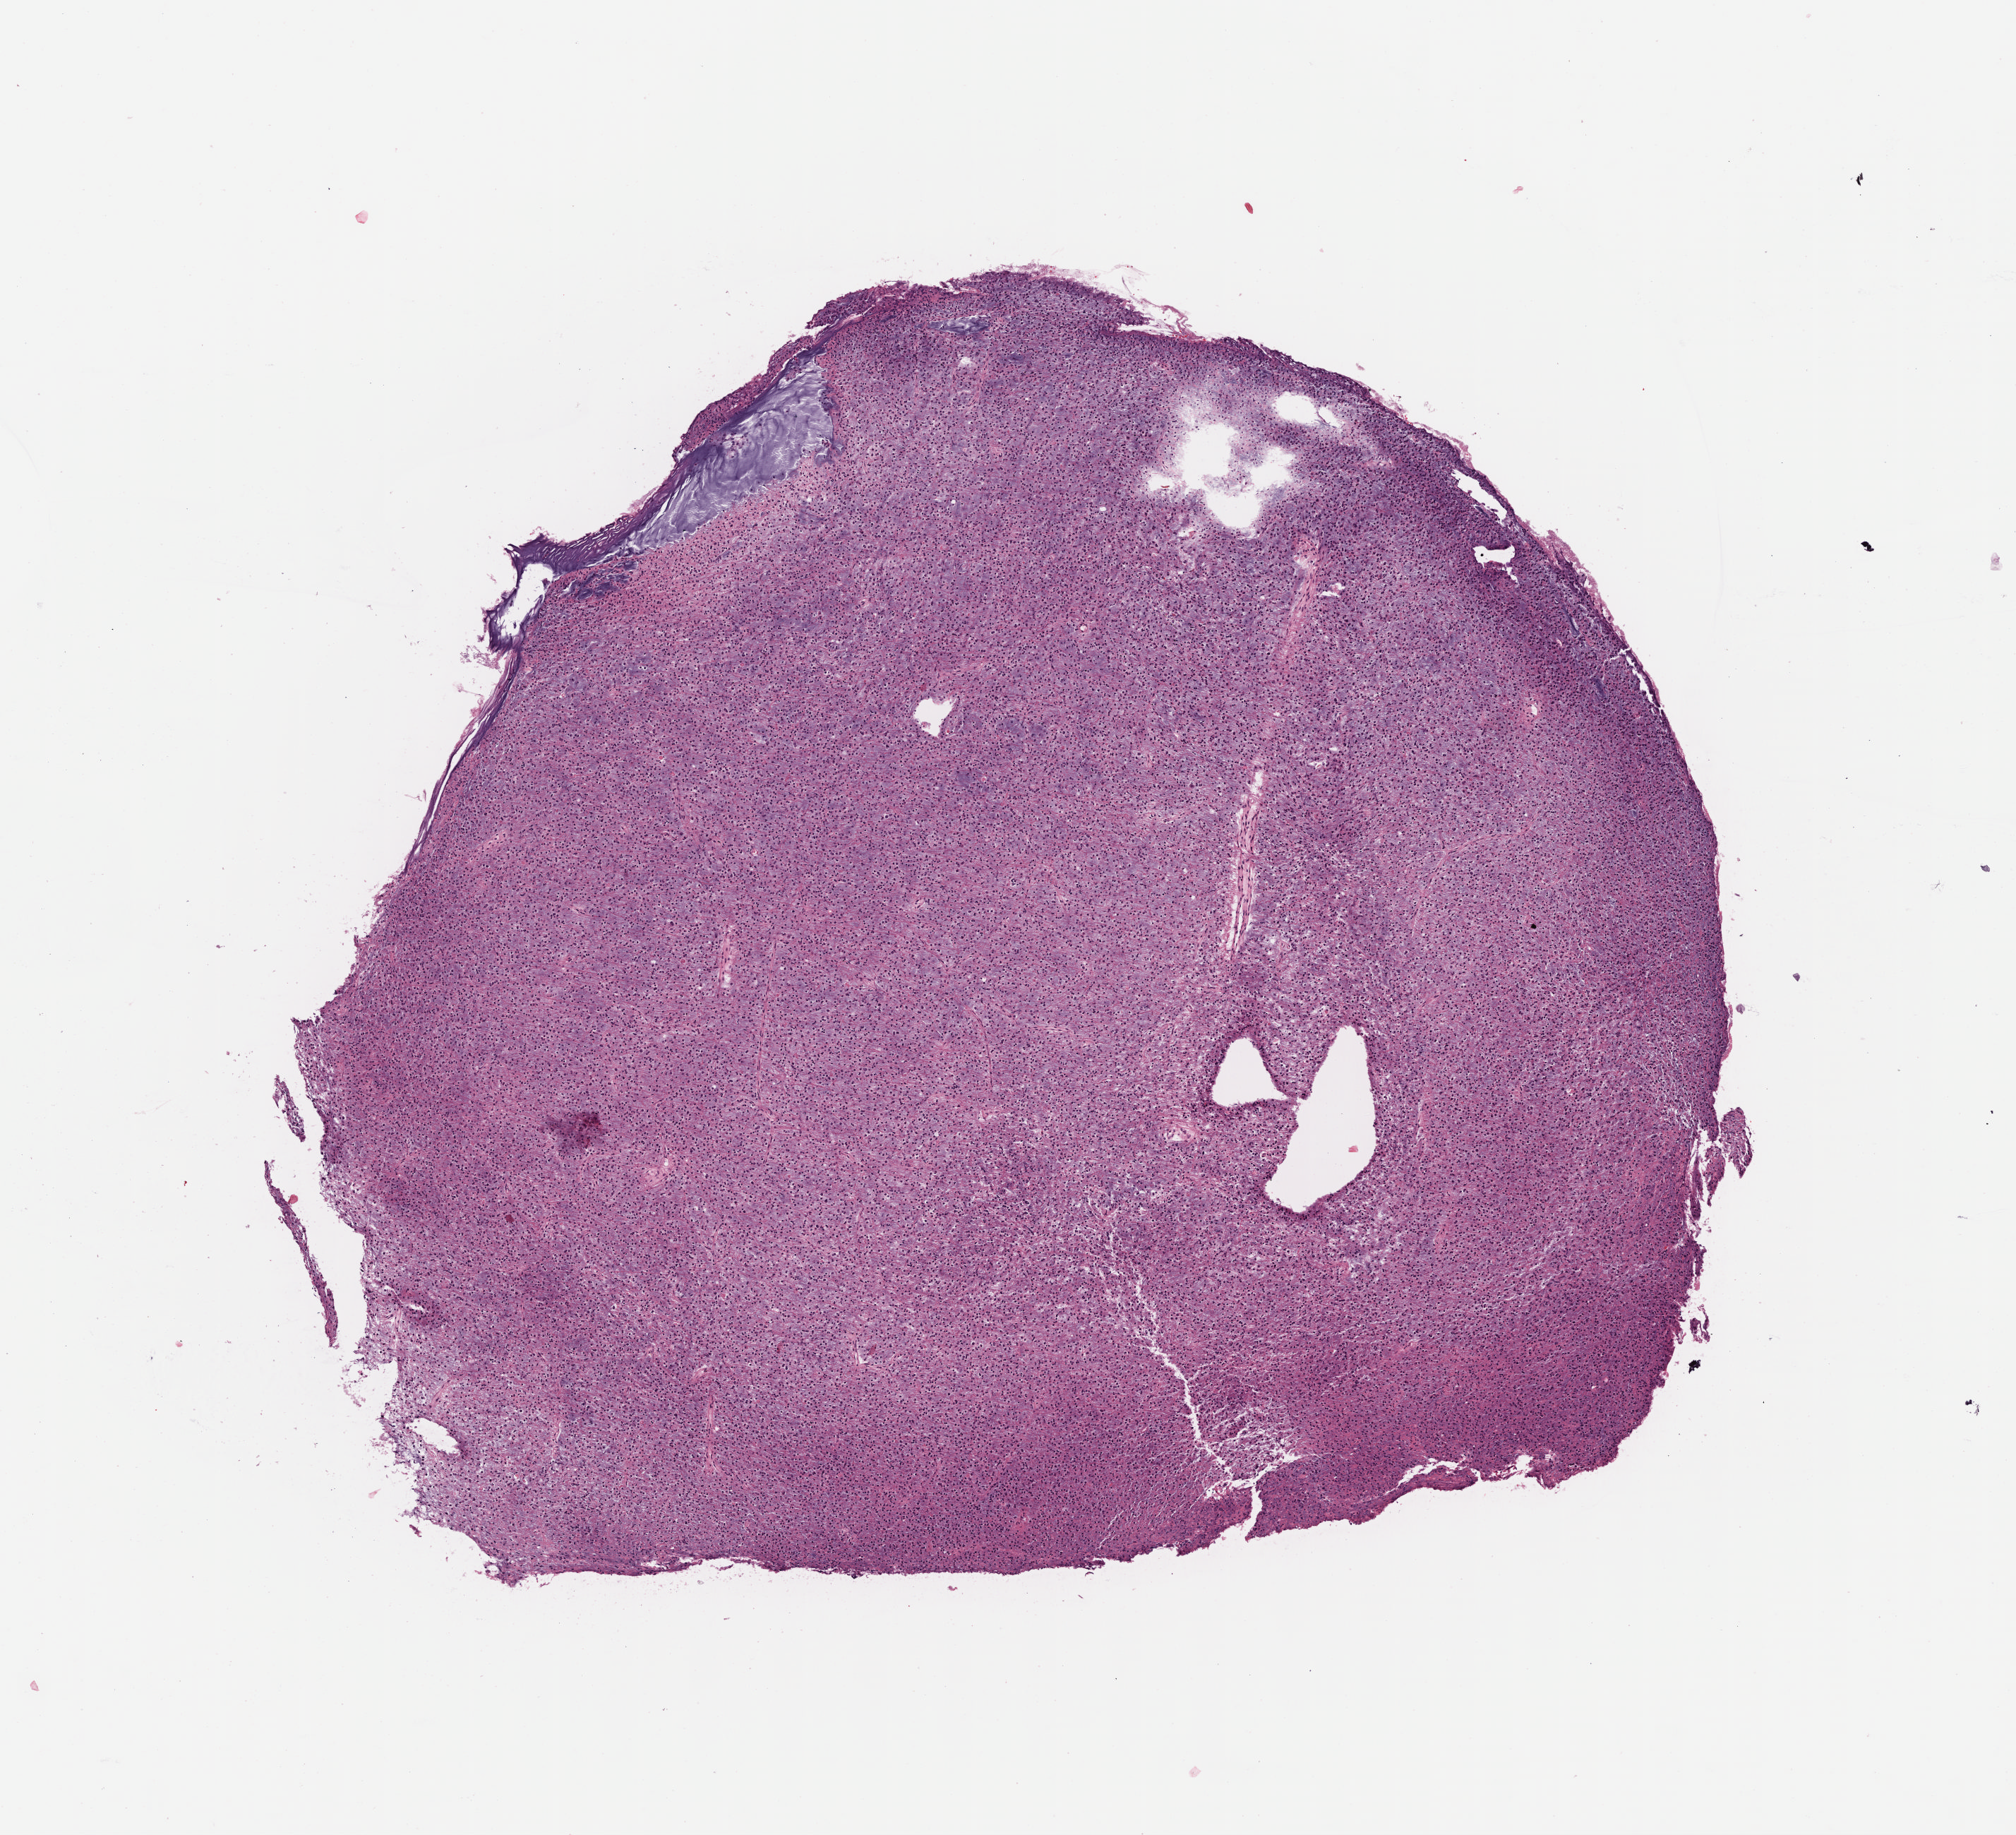
Whole-slide histology image, H&E-stained — a low-resolution overview of the entire scanned area, about 5.6 x 5.1 mm (acquisition: 40x scan); formalin-fixed paraffin-embedded (FFPE) diagnostic section; primary tumour sample from the brain. Patient: male, age at initial diagnosis 30 years. Histologic grade: G2 (moderately differentiated).
Pathologic diagnosis: Mixed glioma.